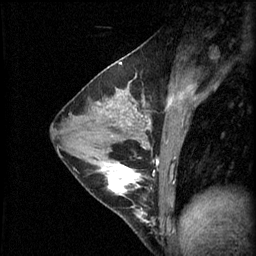
Breast MRI (dynamic contrast-enhanced), one sagittal slice. Position 32 of 60 along the scan axis. 3 images stored at this slice position (order not interpretable as contrast timing). 1.5 T. TE 4.2 ms, TR 11 ms. 2.1 mm slice thickness. 256 × 256 image matrix, field of view 180 × 180 mm. Female patient, age 29 years.
Annotated regions visible in this slice (semi-automatically segmented with operator editing):
- analysis volume of interest (the breast-tissue region the enhancement analysis was run in; not a lesion): bounding box [x1, y1, x2, y2] px = [93, 164, 149, 223]
- tumour enhancement mask (voxels above the 70 % enhancement threshold inside the analysis volume of interest): [97, 164, 144, 219]